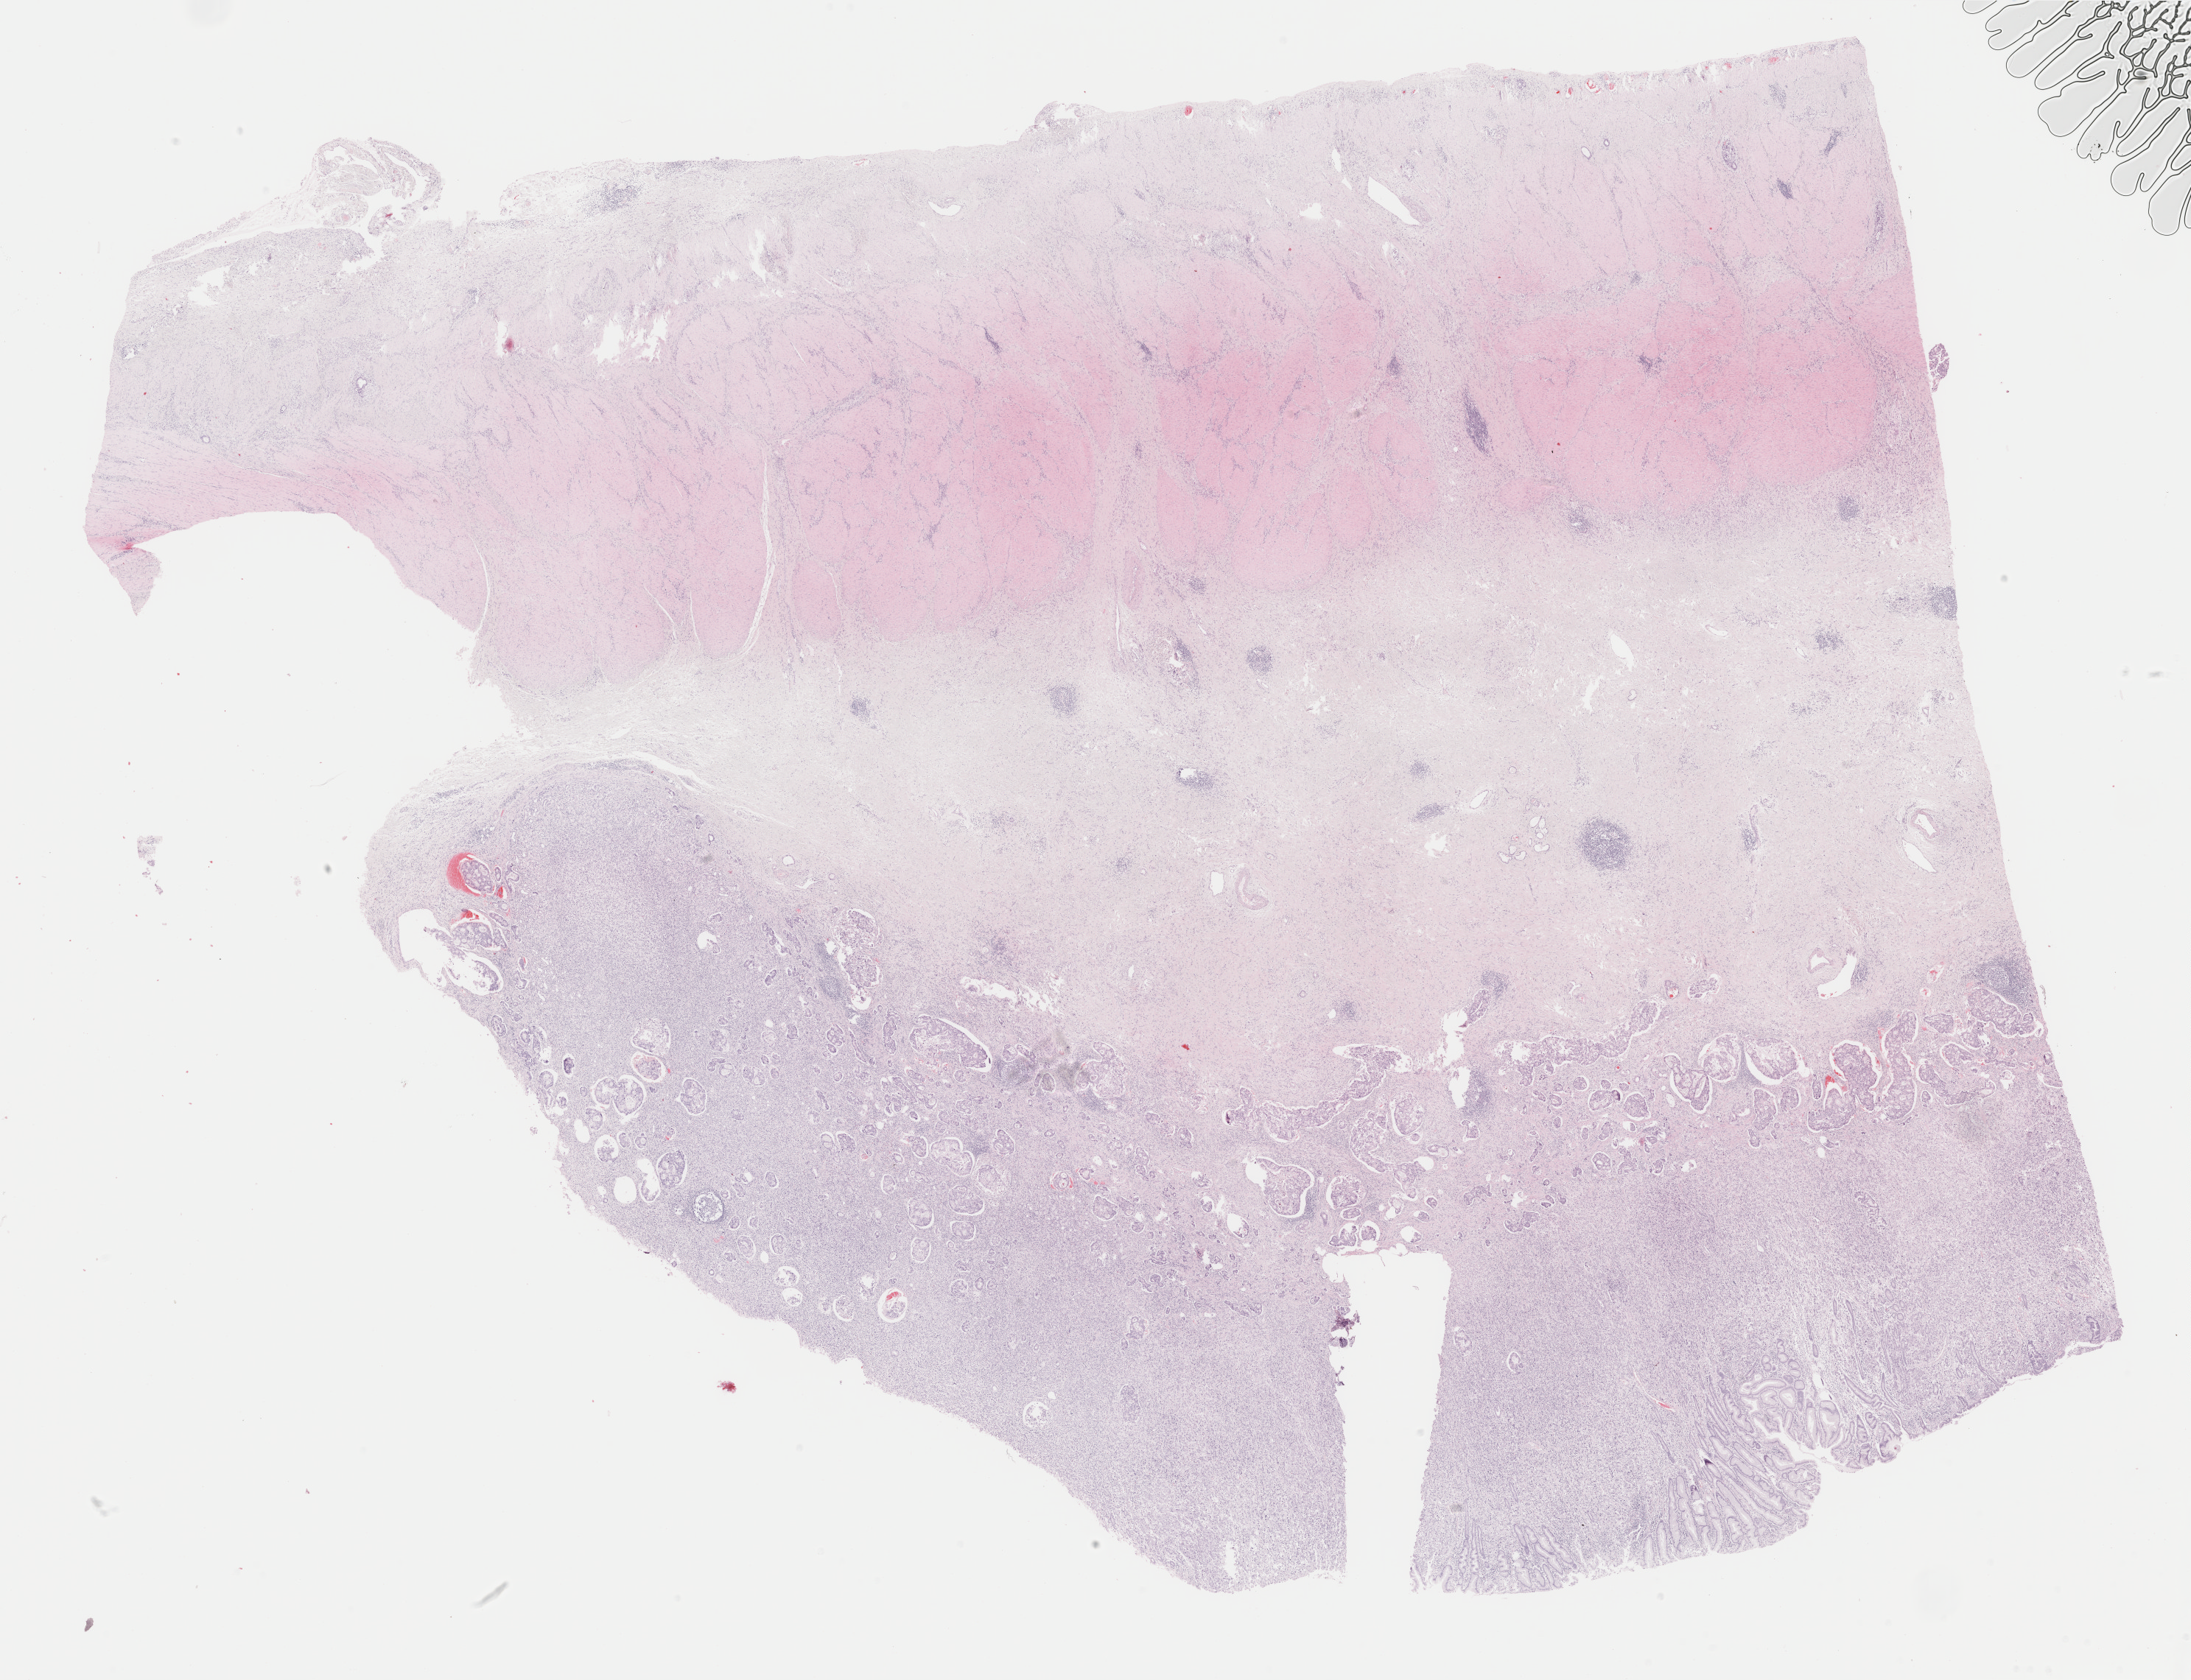
Digitized Hematoxylin and eosin (H&E) stained tissue section (whole slide) — shown as a low-resolution overview of the whole scanned area (about 23.6 x 18.1 mm). FFPE section. Sample: primary tumour, stomach. Female patient; age at initial diagnosis 54 years.
Histologic diagnosis: Tubular adenocarcinoma (gastric antrum).